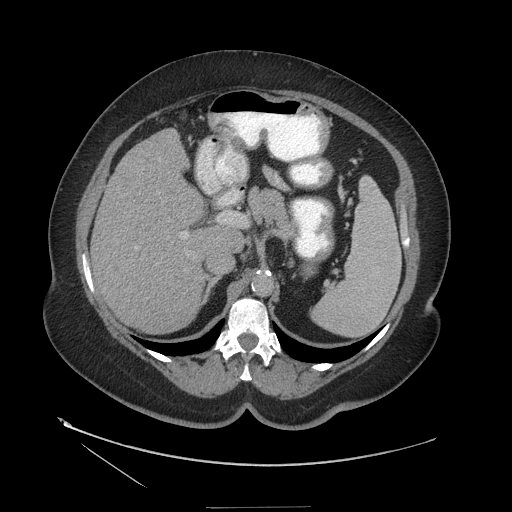
Contrast-enhanced abdominal CT (liver protocol), one axial slice. Soft-tissue window (W 400 / L 40 HU). 2.5 mm slice thickness. 512 × 512 image matrix, field of view 480 × 480 mm. From the clinical record (not read from this slice): diagnosis: hepatocellular carcinoma (patient treated with transarterial chemoembolisation; whether this scan precedes or follows treatment is not stated here); TNM stage (as recorded): Stage-II; Child-Pugh class: A; tumour nodularity: multinodular; tumour size: 3 cm.
Annotated regions visible in this slice (semi-automatically segmented with operator editing):
- liver parenchyma outside the tumour (the mass and vessels are separate outlines, so this box may not span the whole liver): bounding box [x1, y1, x2, y2] px = [92, 128, 227, 332]
- liver vessels: [135, 232, 188, 248]